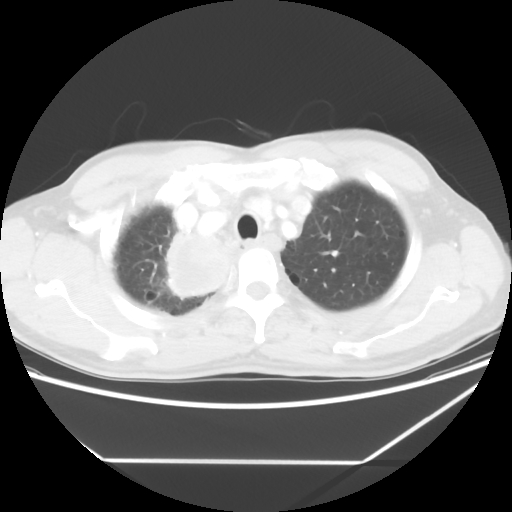
Chest CT, one axial slice. Position 51 of 60 along the scan axis. Reconstruction kernel STANDARD. Lung window (W 1500 / L -600 HU). 5 mm slice thickness. 512 × 512 image matrix. Male patient, age 58 years. From the clinical record (not read from this slice): clinical TNM (as recorded): T2 N2 M0.
Annotated regions visible in this slice (bounding box drawn by a radiologist):
- lung tumour (recorded histology: squamous cell carcinoma): bounding box [x1, y1, x2, y2] px = [152, 221, 237, 302]